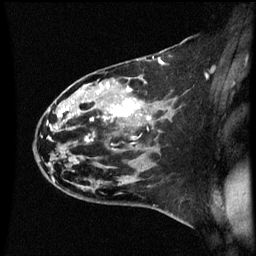
Breast MRI (dynamic contrast-enhanced), one sagittal slice. Position 37 of 60 along the scan axis. Dynamic contrast-enhanced series, image 2 of 3 at this slice position (ordered by acquisition). 1.5 T. TE 4.2 ms, TR 8.9 ms. 2 mm slice thickness. 256 × 256 image matrix. Female patient, age 44 years. Case-level facts recorded for this patient, not image findings: setting: breast cancer imaged before/during neoadjuvant chemotherapy; receptor status: HR-positive, HER2-negative.
Outlined on this slice (semi-automatic segmentation, software-assisted and operator-edited):
- analysis volume of interest (the breast-tissue region the enhancement analysis was run in; not a lesion): bounding box (x1, y1, x2, y2) in pixels: (43, 78, 153, 189)
- tumour enhancement mask (voxels above the 70 % enhancement threshold inside the analysis volume of interest): (47, 84, 149, 127)